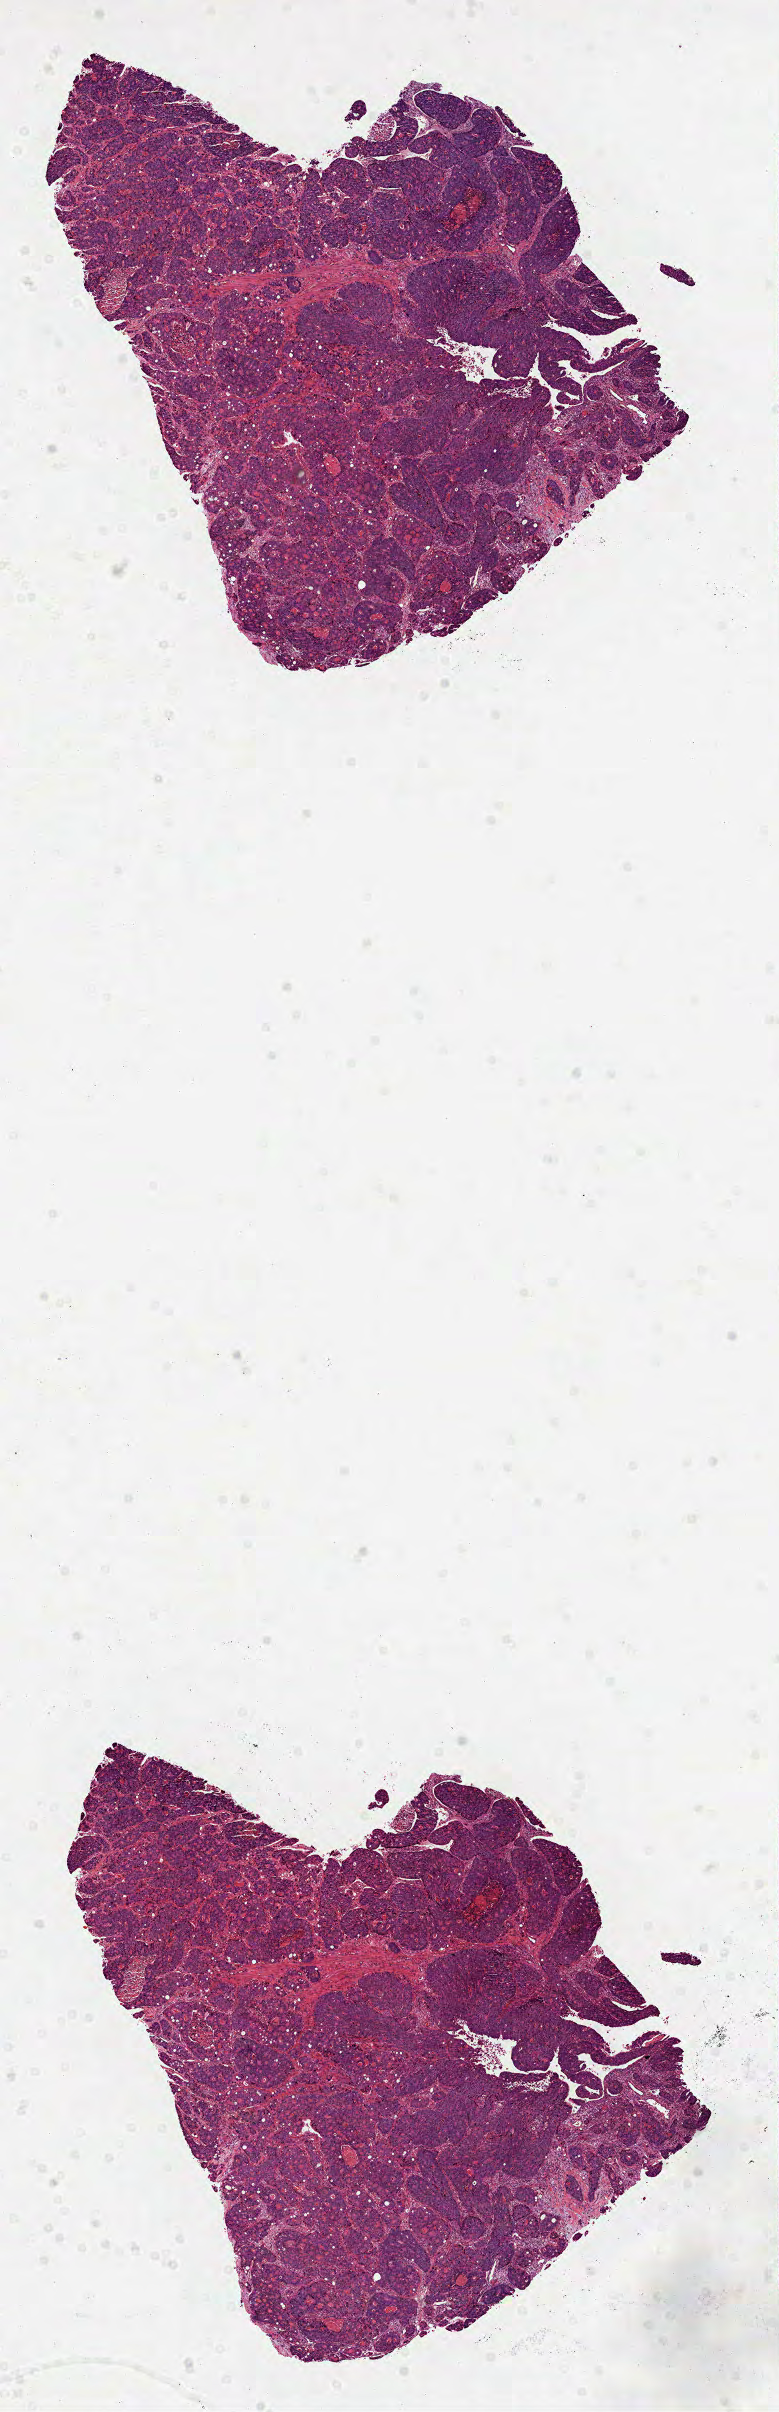
Digitized H&E-stained tissue section (whole slide) — low-resolution overview of the scanned area, about 6.3 x 19.5 mm (acquisition: 40x scan); formalin-fixed paraffin-embedded (FFPE) diagnostic section; sample: primary tumour, colon. Patient: male, age at initial diagnosis 46 years.
AJCC pathologic stage: IVA. Lymph nodes positive (case pathology): 7 of 13 examined. Histologic diagnosis: Adenocarcinoma, NOS (splenic flexure of colon).